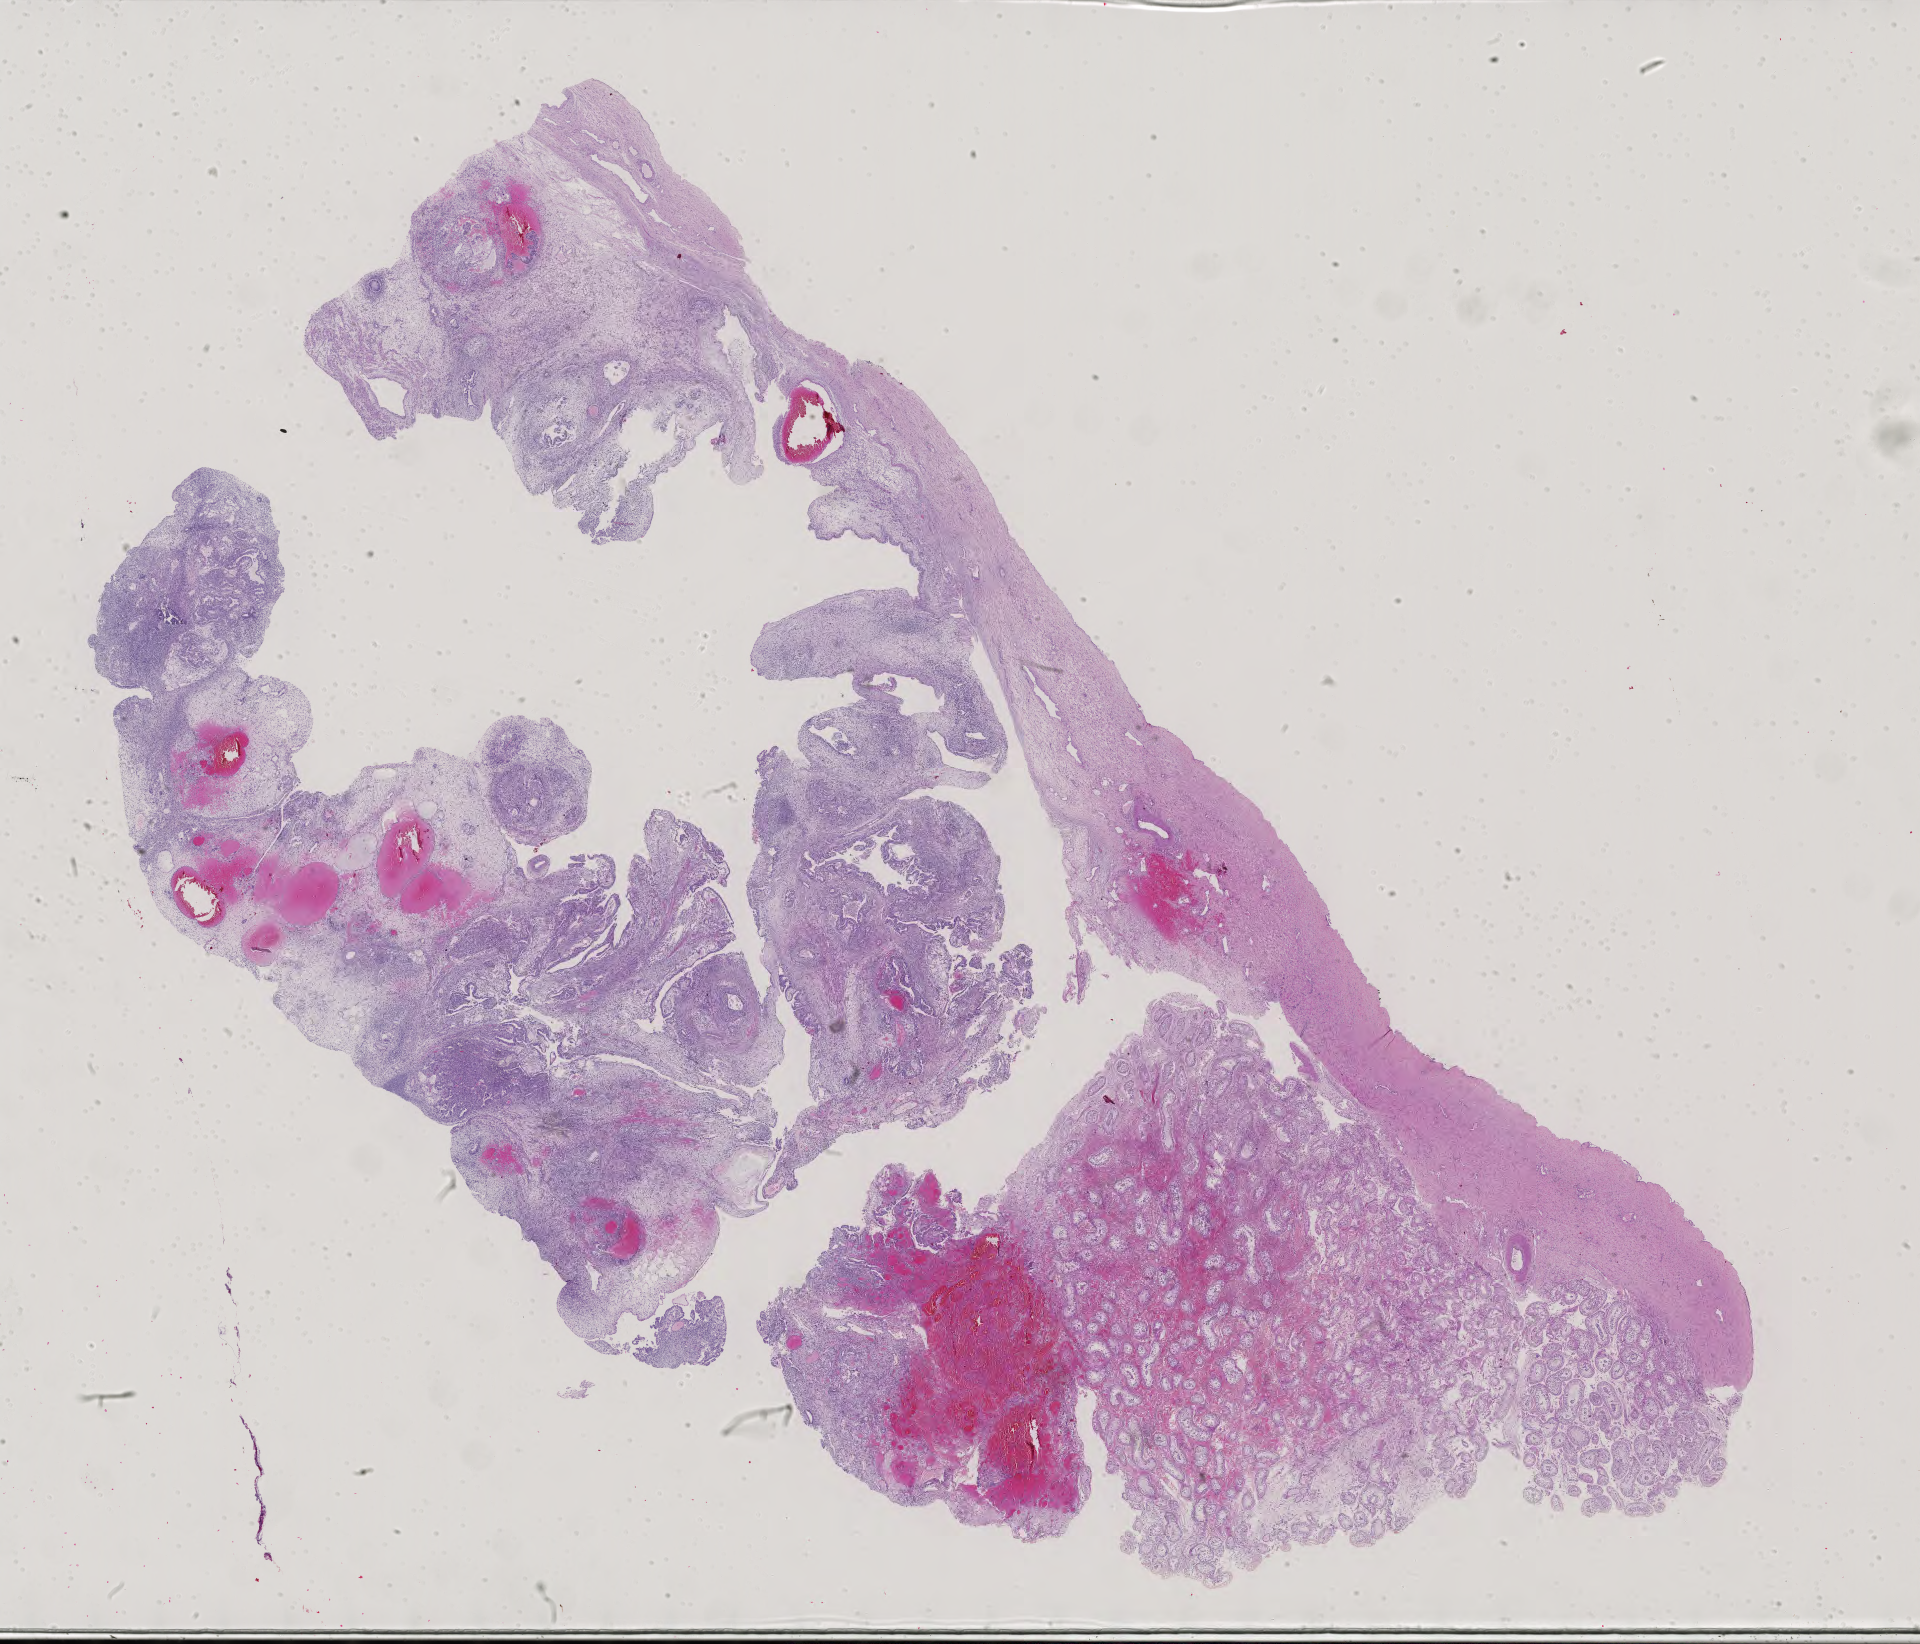
H&E whole-slide image — whole scanned area (about 28.0 x 24.0 mm, from a 40x scan) shown as a low-resolution overview, formalin-fixed paraffin-embedded (FFPE) diagnostic section, sample: primary tumour, testis. Male, age 39 years at initial diagnosis.
* AJCC pathologic stage: IIIB (5th edition)
* histologic diagnosis: Mixed germ cell tumor
* laterality: right